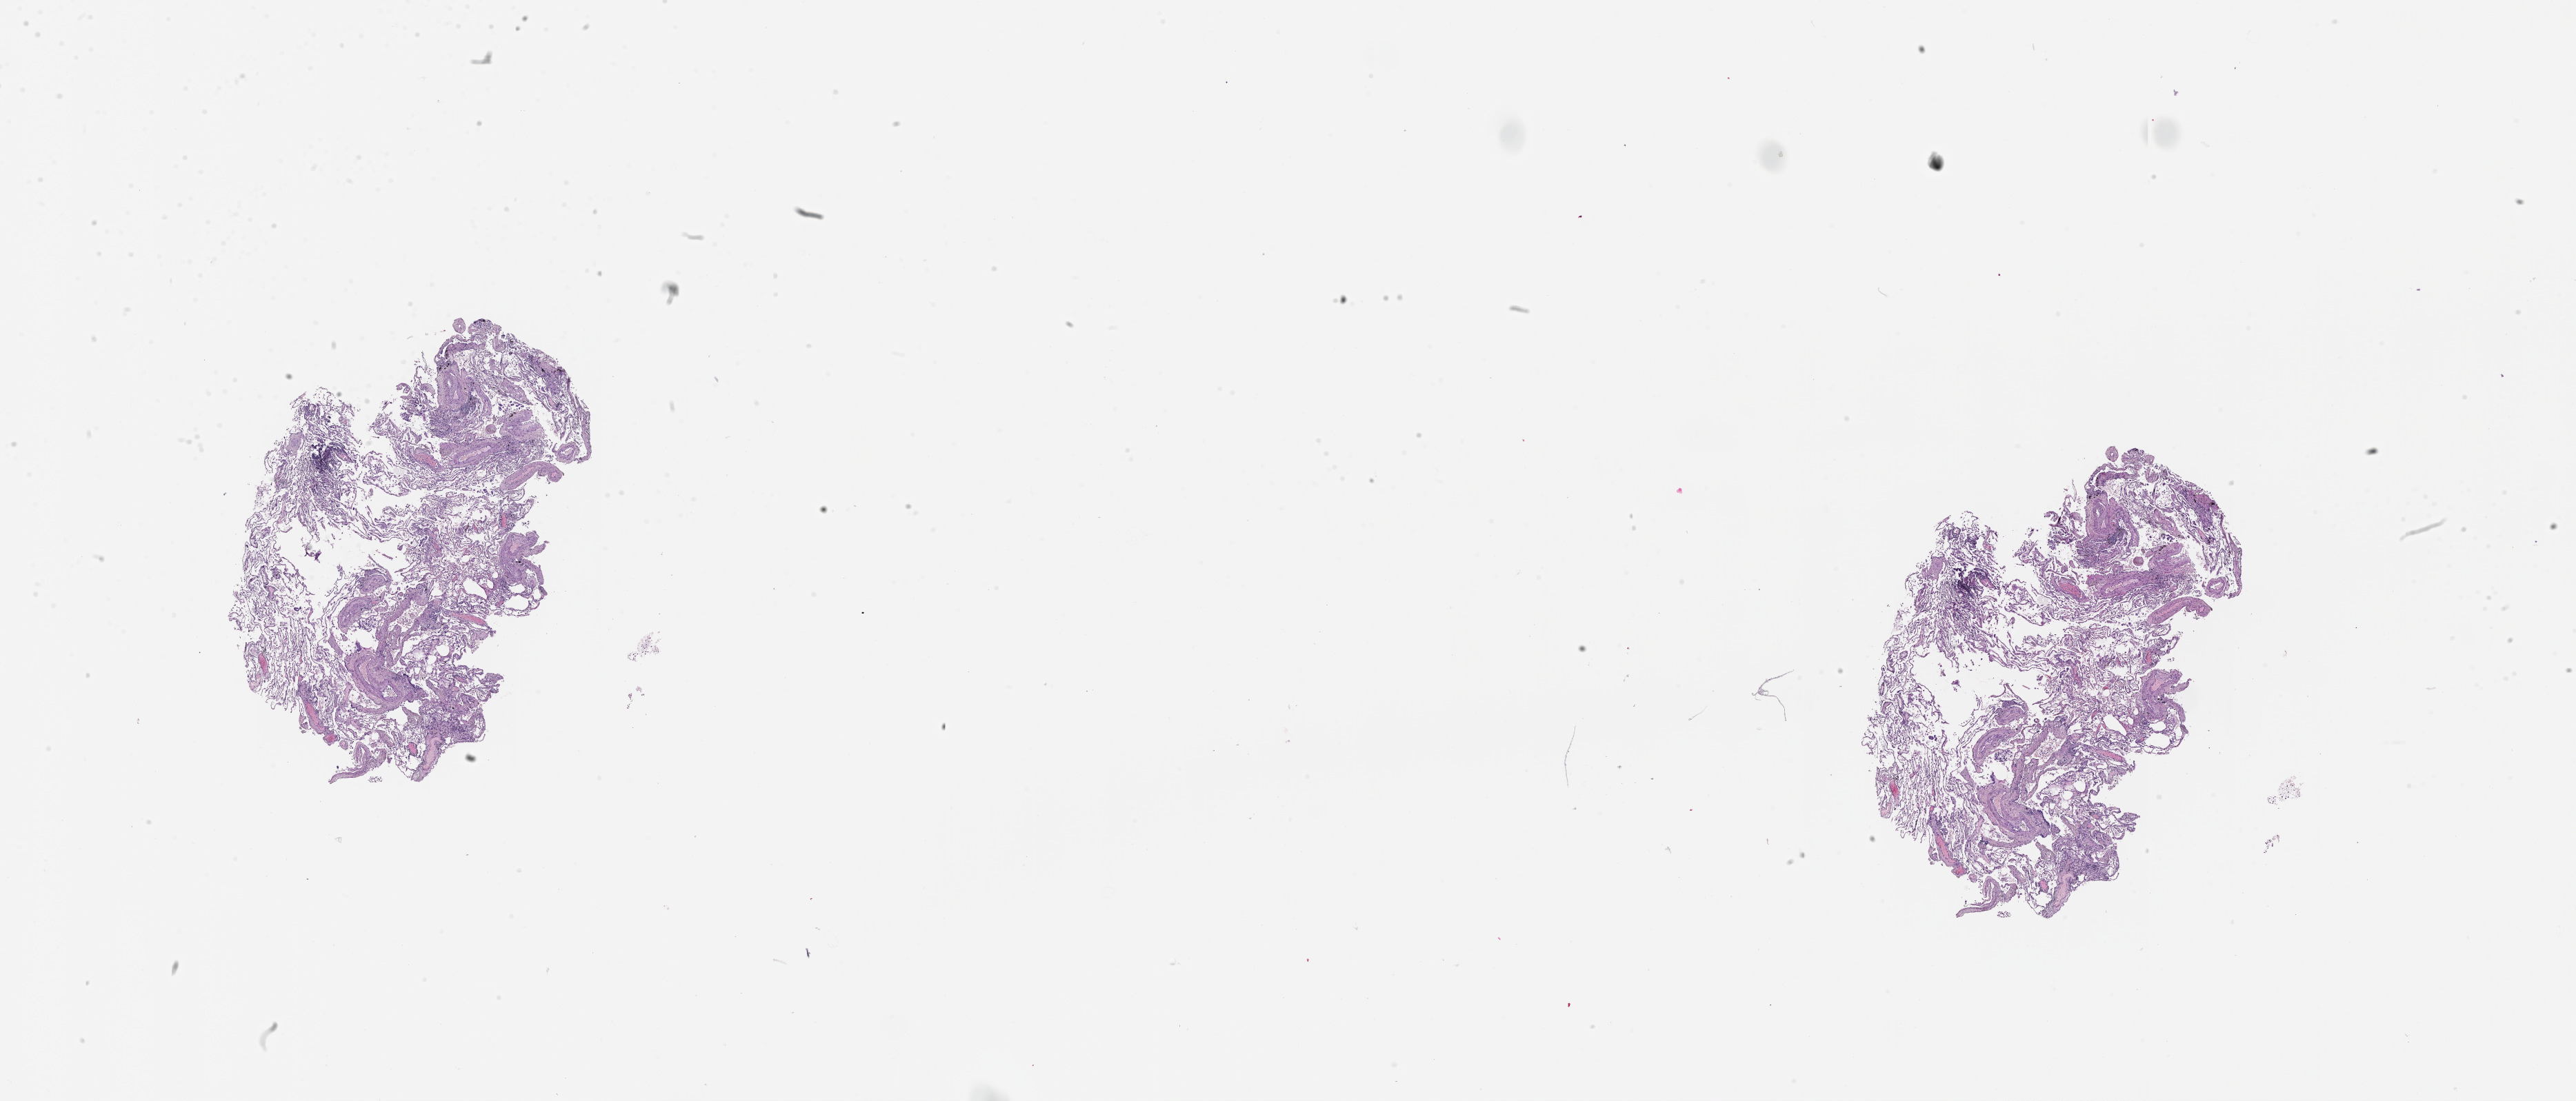
Whole-slide histology image, H&E, low-resolution overview of the scanned area, about 30.1 x 12.9 mm. Normal (non-tumour) tissue sample, sampled site: lung. 67-year-old male patient.
This section: normal (non-tumour) tissue from the same patient. Patient diagnosis: Adenocarcinoma, NOS.